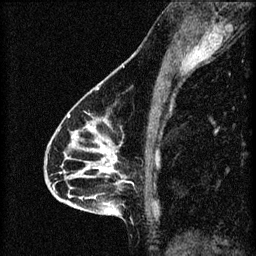
Breast MRI (dynamic contrast-enhanced), one sagittal slice. Slice 34 of 60 in the series (ordered by position). 3 images stored at this slice position (order not interpretable as contrast timing). 1.5 T. TE 4.2 ms, TR 8.2 ms. 2 mm slice thickness. 256 × 256 image matrix, field of view 180 × 180 mm. Female patient, age 46 years.
Annotated regions visible in this slice (semi-automatically segmented with operator editing):
- analysis volume of interest (the breast-tissue region the enhancement analysis was run in; not a lesion): bounding box <55,114,148,209> (left, top, right, bottom; pixels)
- tumour enhancement mask (voxels above the 70 % enhancement threshold inside the analysis volume of interest): <68,116,123,183>